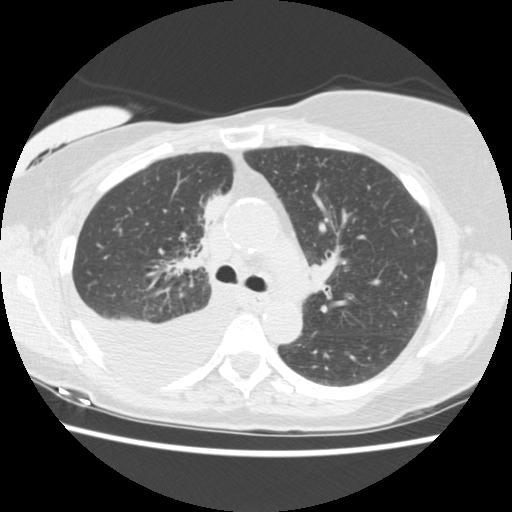
Low-dose screening chest CT, axial slice. Third annual screen. Lung window (W 1500 / L -600 HU). Standard (soft-tissue) reconstruction kernel (STANDARD). Slice 60 of 157 in the series. 512 × 512 image matrix. Female participant, aged 56 years at enrolment. Current smoker at enrolment.
Lesion marked by an expert reader, bounding box <182,185,242,251> (left, top, right, bottom; pixels). The screening reader recorded 2 non-calcified nodules or masses ≥4 mm on this exam (right middle lobe, right lower lobe); which of them this box marks is not recorded. Official screen result: positive, other. Lung cancer was diagnosed 160 days after this screen: adenocarcinoma, NOS, right upper lobe, stage IIIB (AJCC 6th edition), 8 mm at pathology.